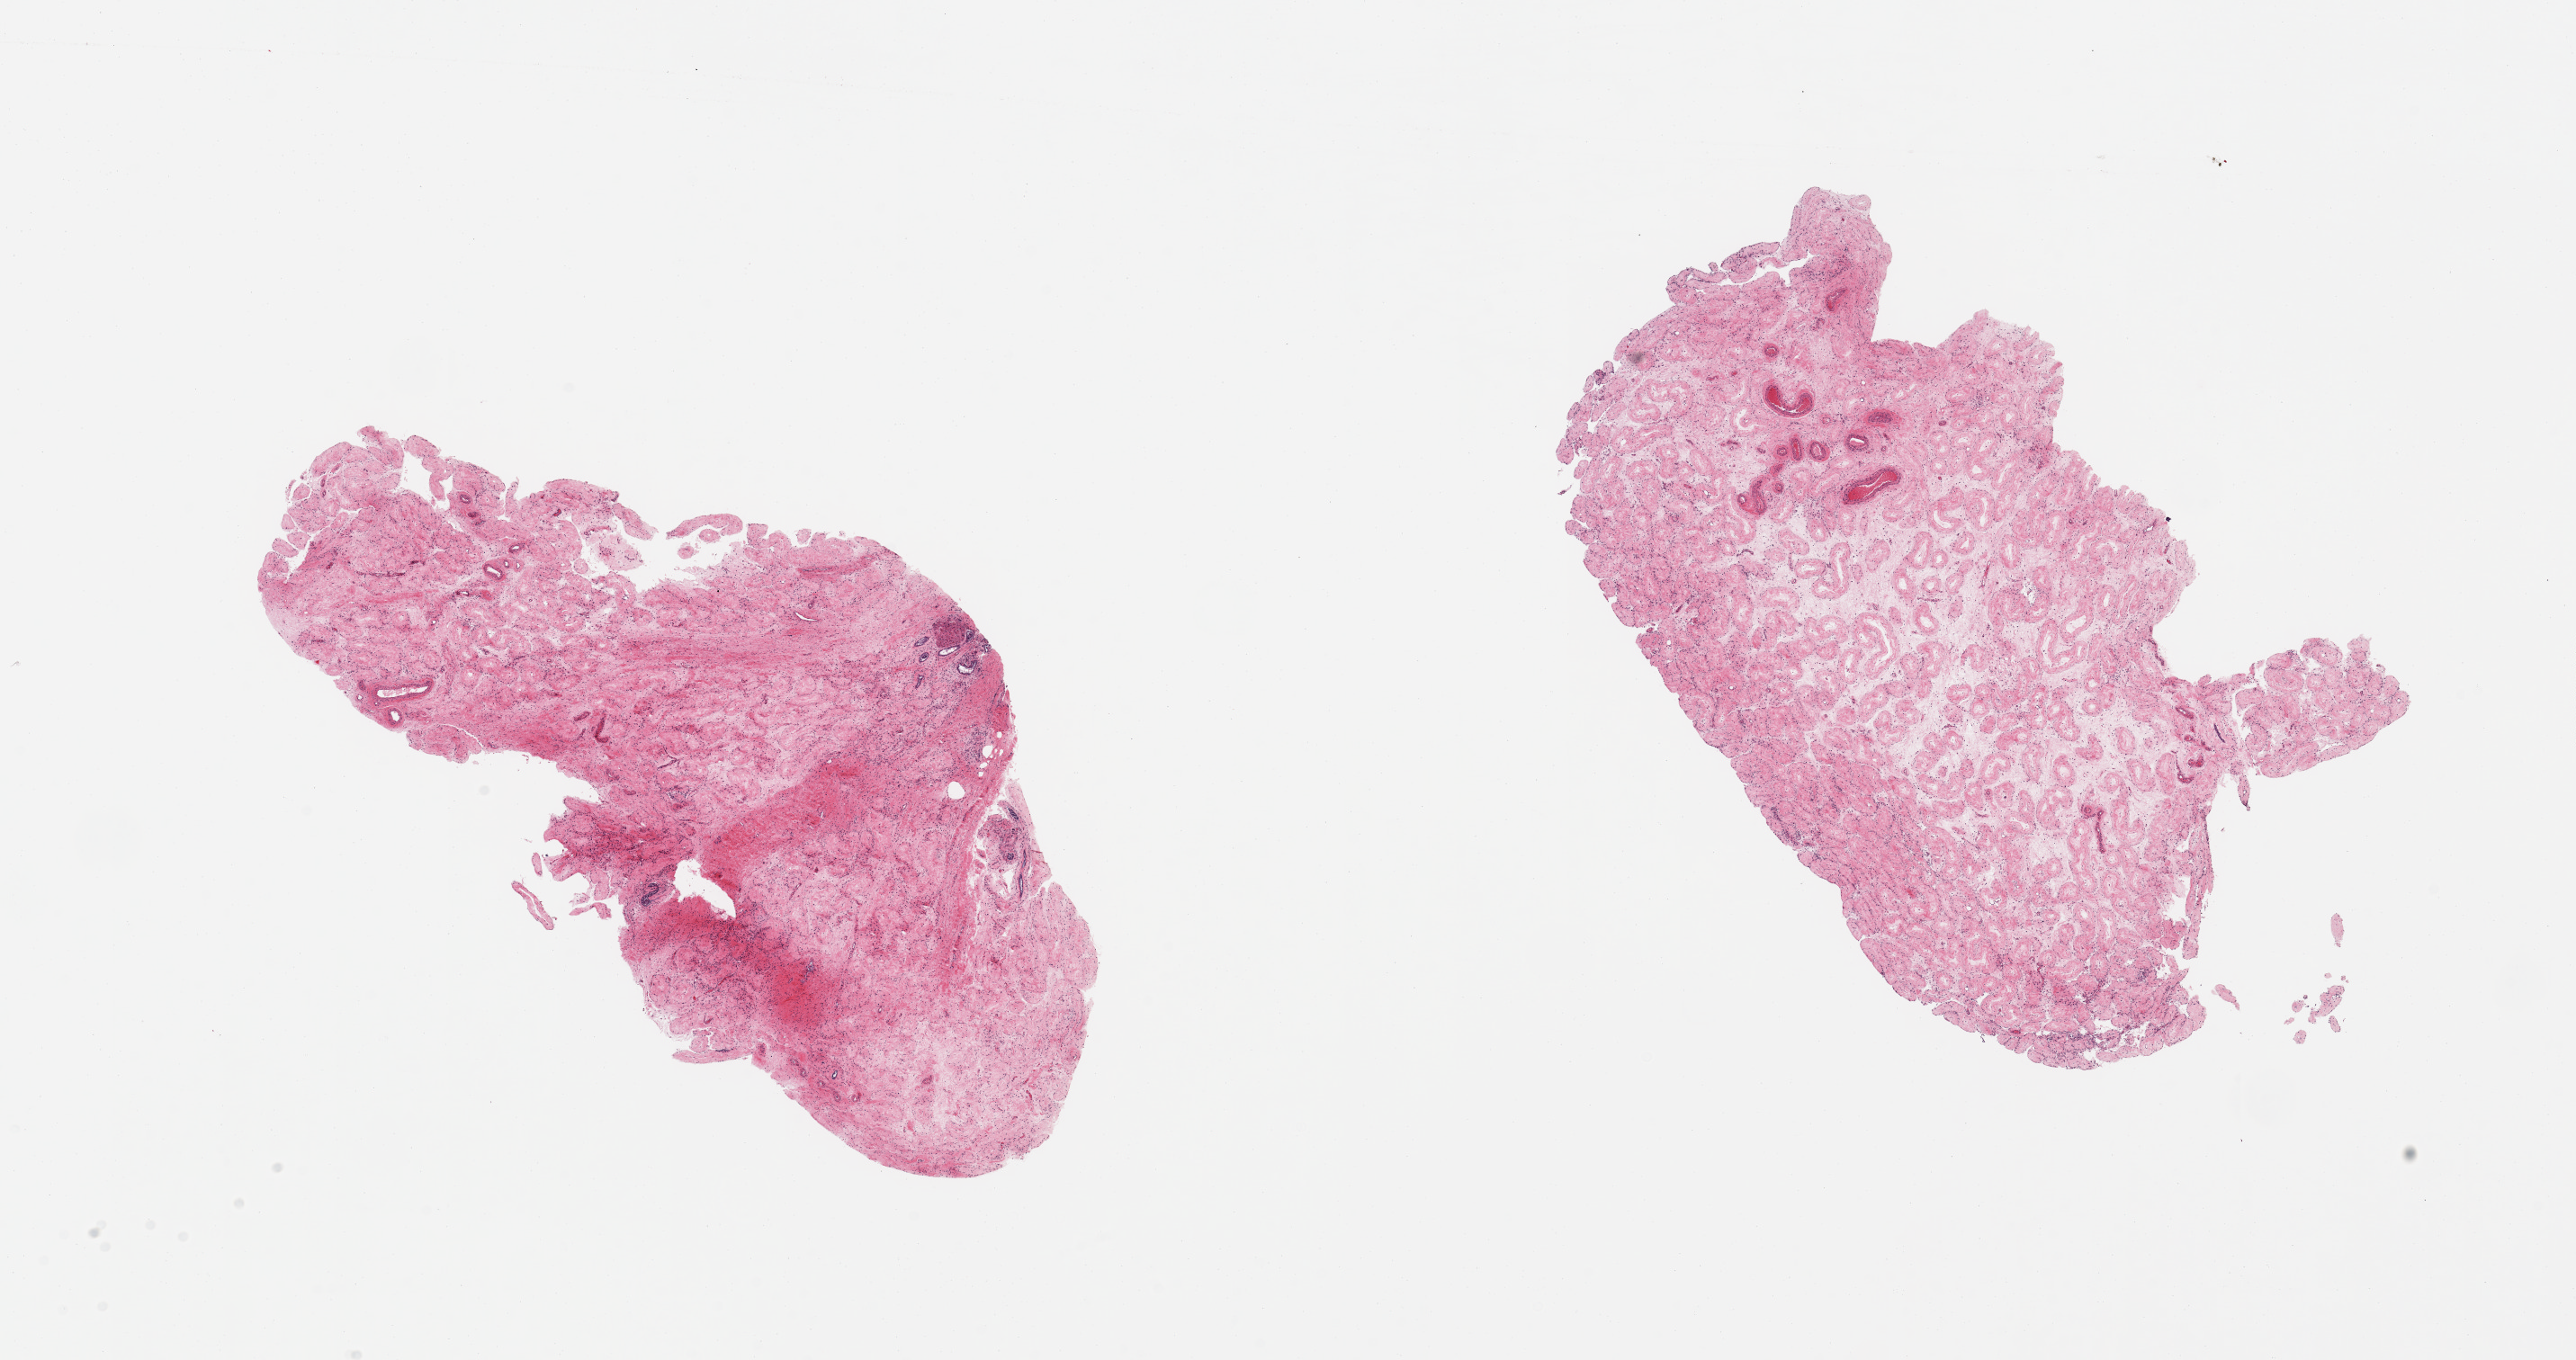
Digitized hematoxylin and eosin (H&E)-stained section — shown as a low-resolution overview of the whole scanned area (about 22.6 x 12.0 mm); PAXgene-fixed, paraffin-embedded tissue; target tissue: testis; donor tissue sample. Male donor.
* reviewer comment on this tissue sample: 2 pieces; atrophic; no spermatogenesis; no Sertoli cells; hyalinized tubules; rare Leydig cells